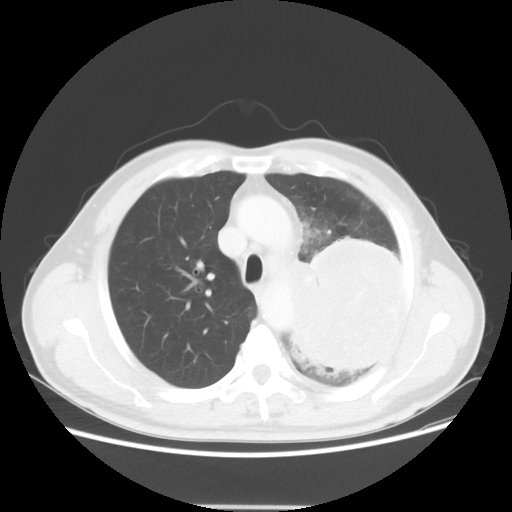
Chest CT, one axial slice. Position 39 of 53 along the scan axis. 100 kVp. Lung window (W 1500 / L -600 HU). 512 × 512 image matrix, field of view 391 × 391 mm. Male patient, age 60 years. Case-level facts recorded for this patient, not image findings: clinical TNM (as recorded): T4 N1 M1a; histopathological grade: G3.
Structures marked on this image (rectangle marked by the reading radiologist):
- lung tumour (recorded histology: large cell carcinoma): bounding box [x1, y1, x2, y2] px = [277, 231, 426, 385]